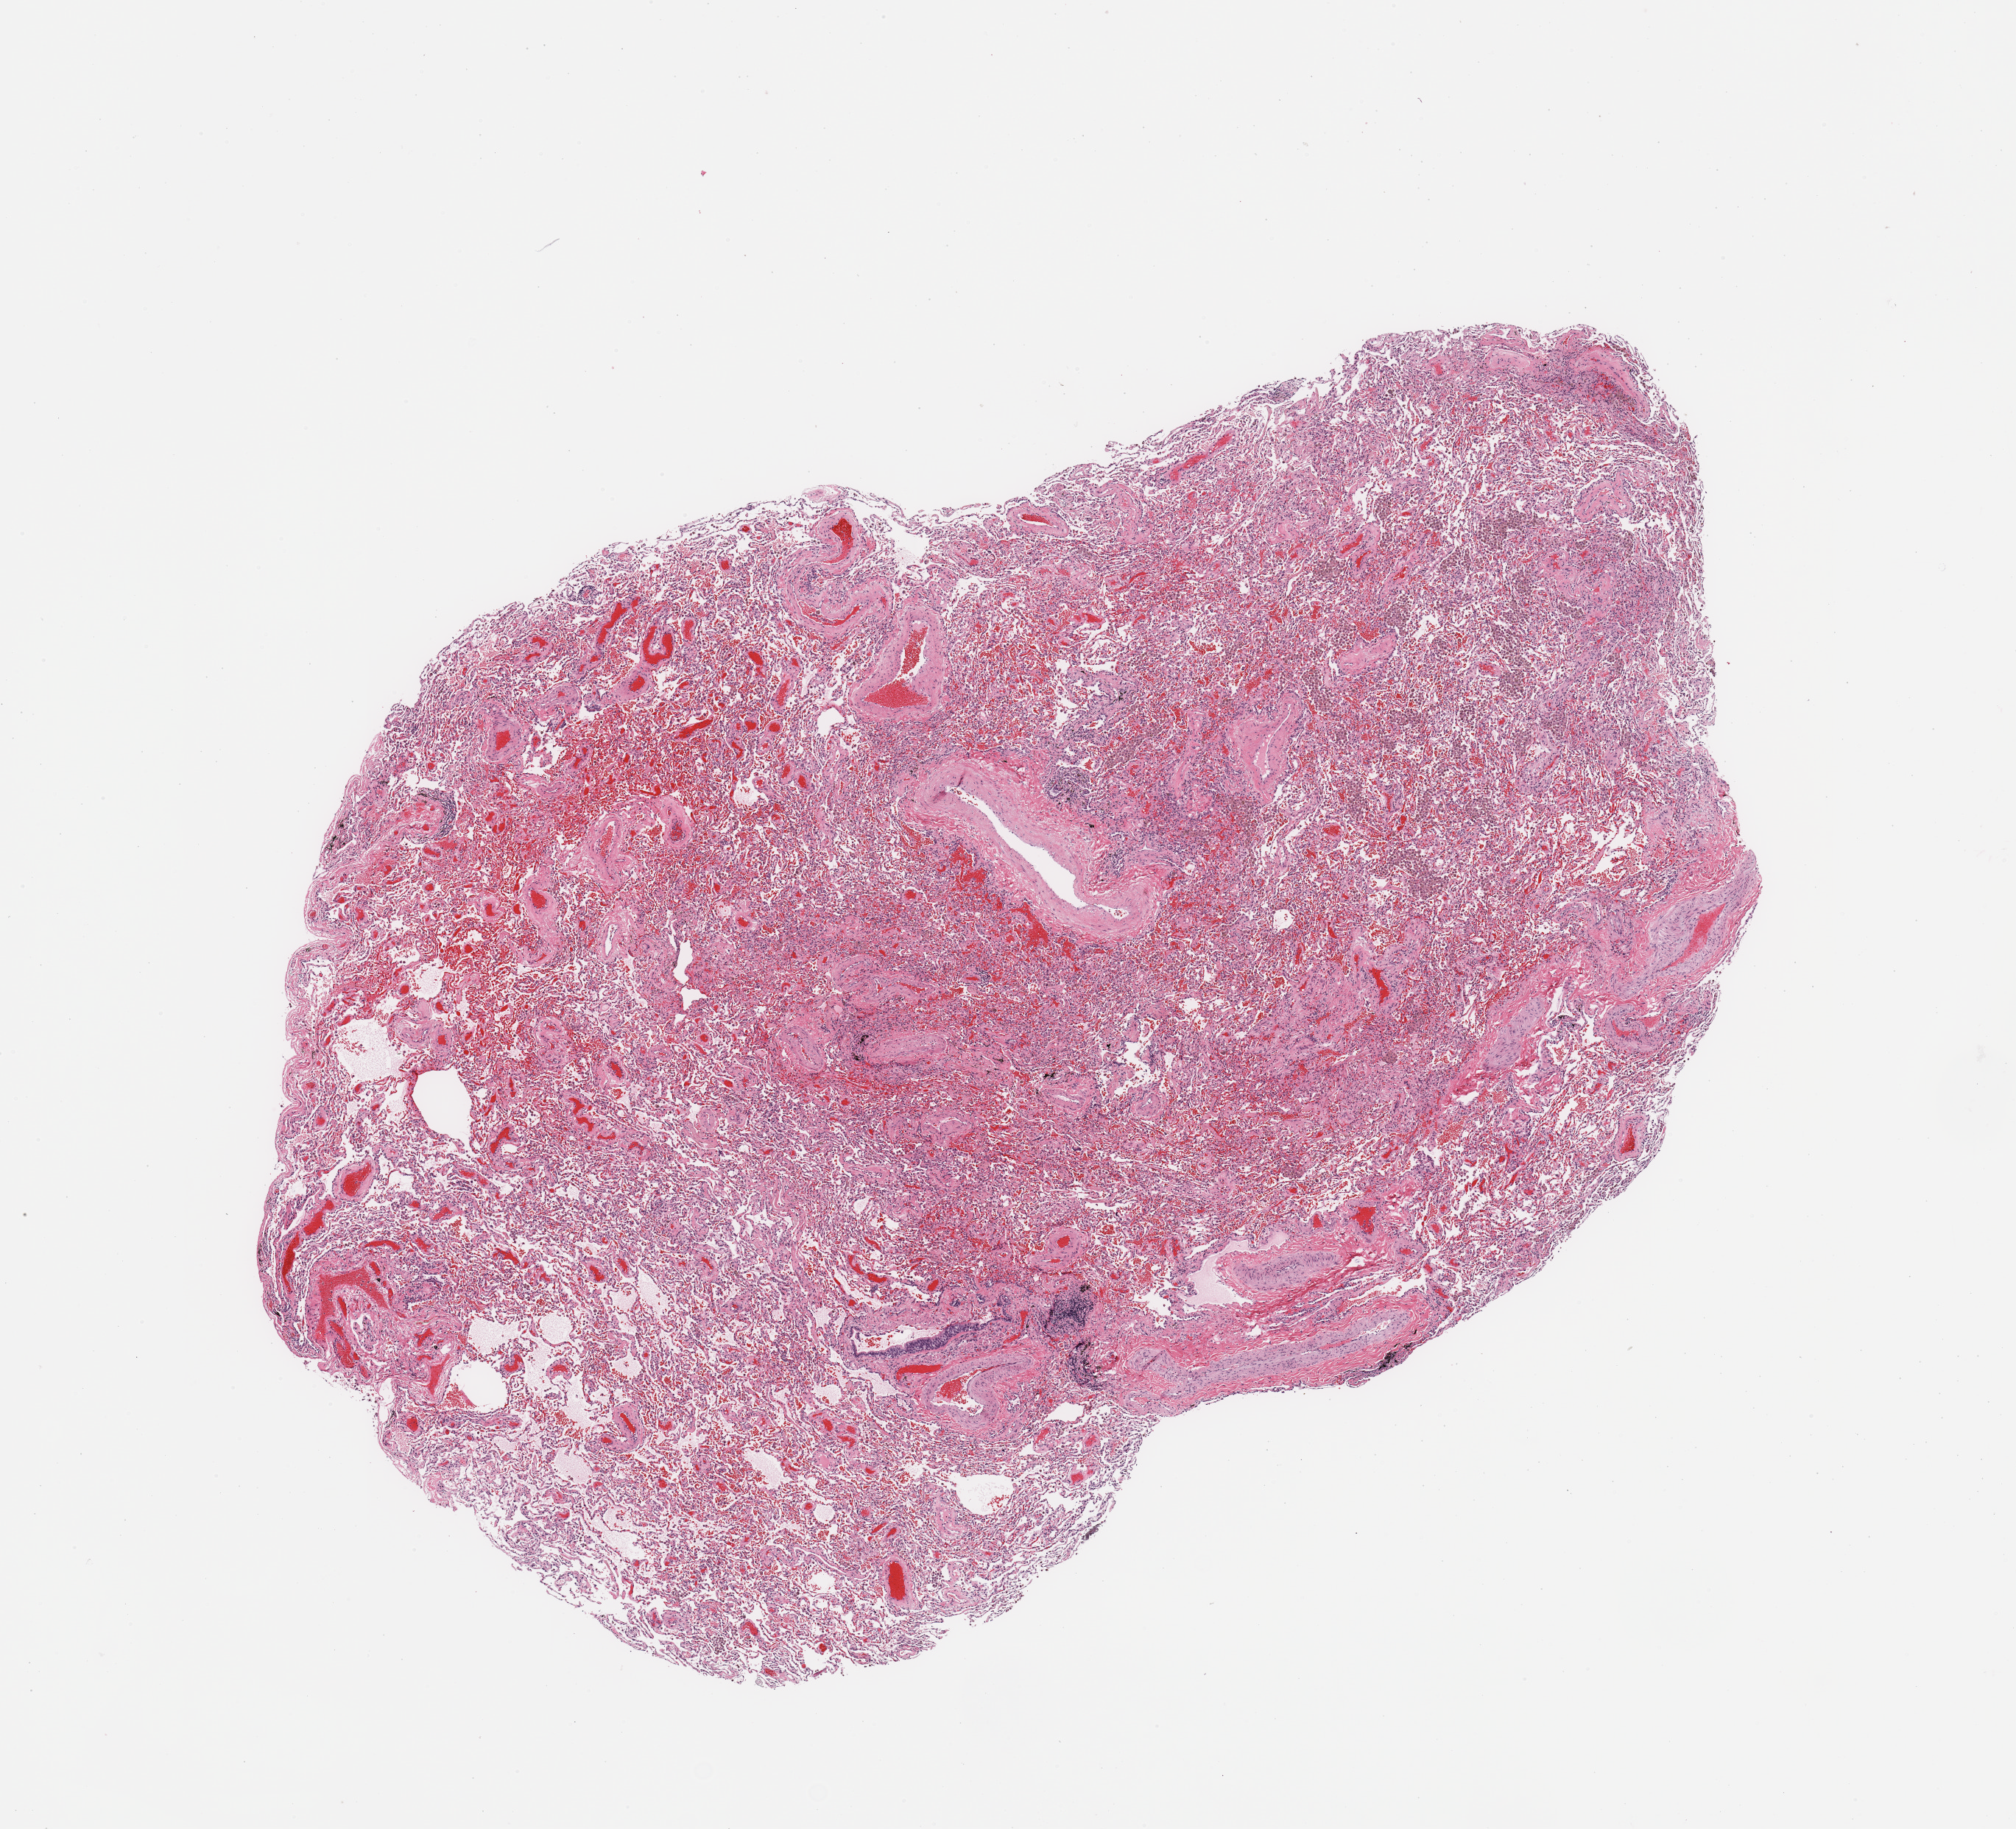
Hematoxylin and eosin (H&E) stained whole-slide image — a low-resolution overview of the entire scanned area, about 10.8 x 9.8 mm (acquisition: 20x scan). Normal (non-tumour) tissue sample, sampled site: lung. Patient: female, age 59 years.
This section: normal (non-tumour) tissue from the same patient. Patient diagnosis: Adenocarcinoma, NOS.